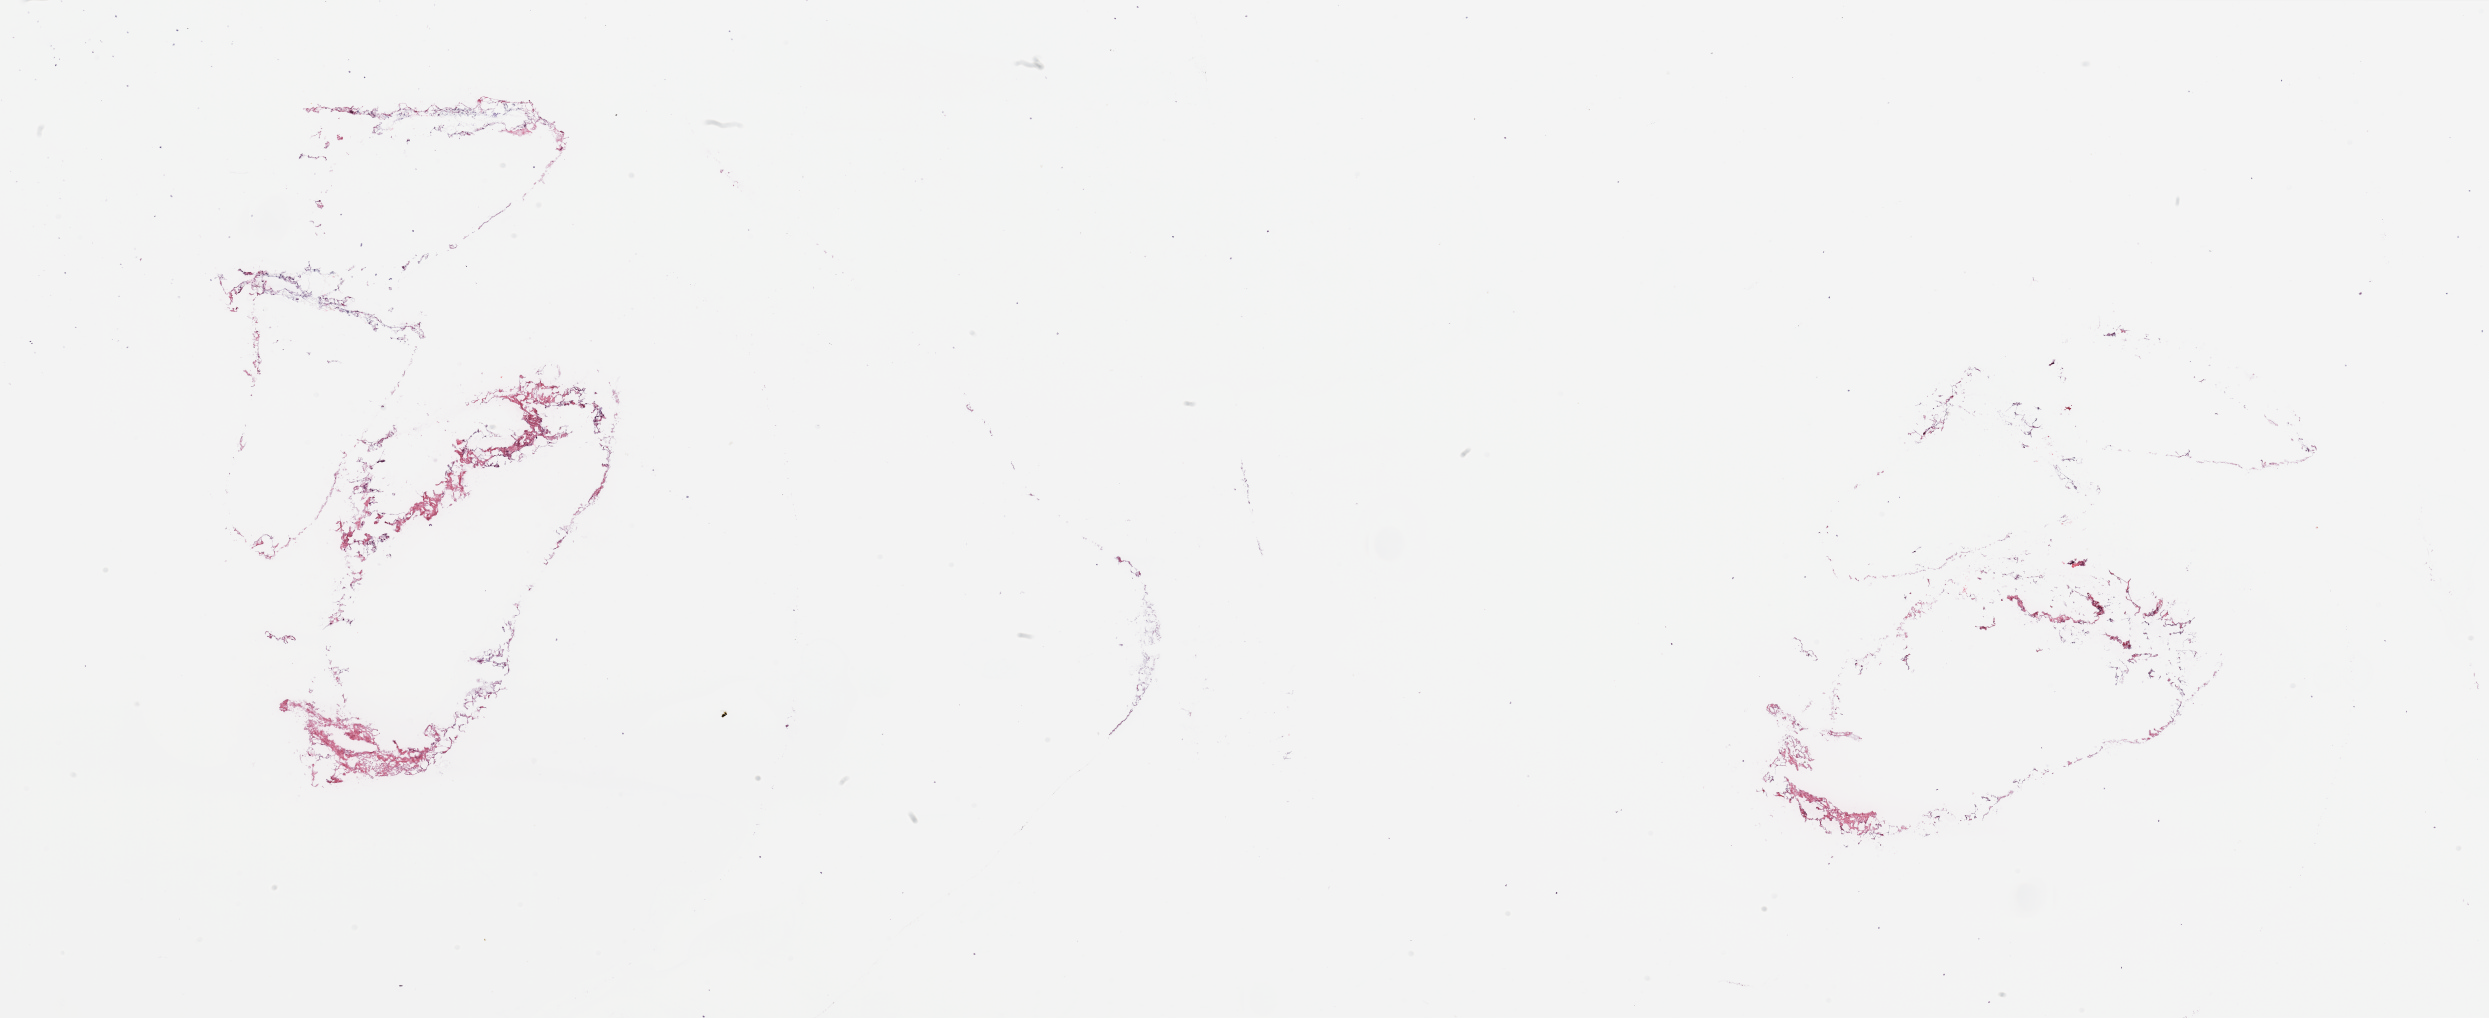
Whole-slide histology image, H&E-stained — low-resolution overview of the scanned area, about 39.4 x 16.1 mm. Breast, tissue type not recorded.
Patient diagnosis (cohort enrolment): breast cancer (breast).